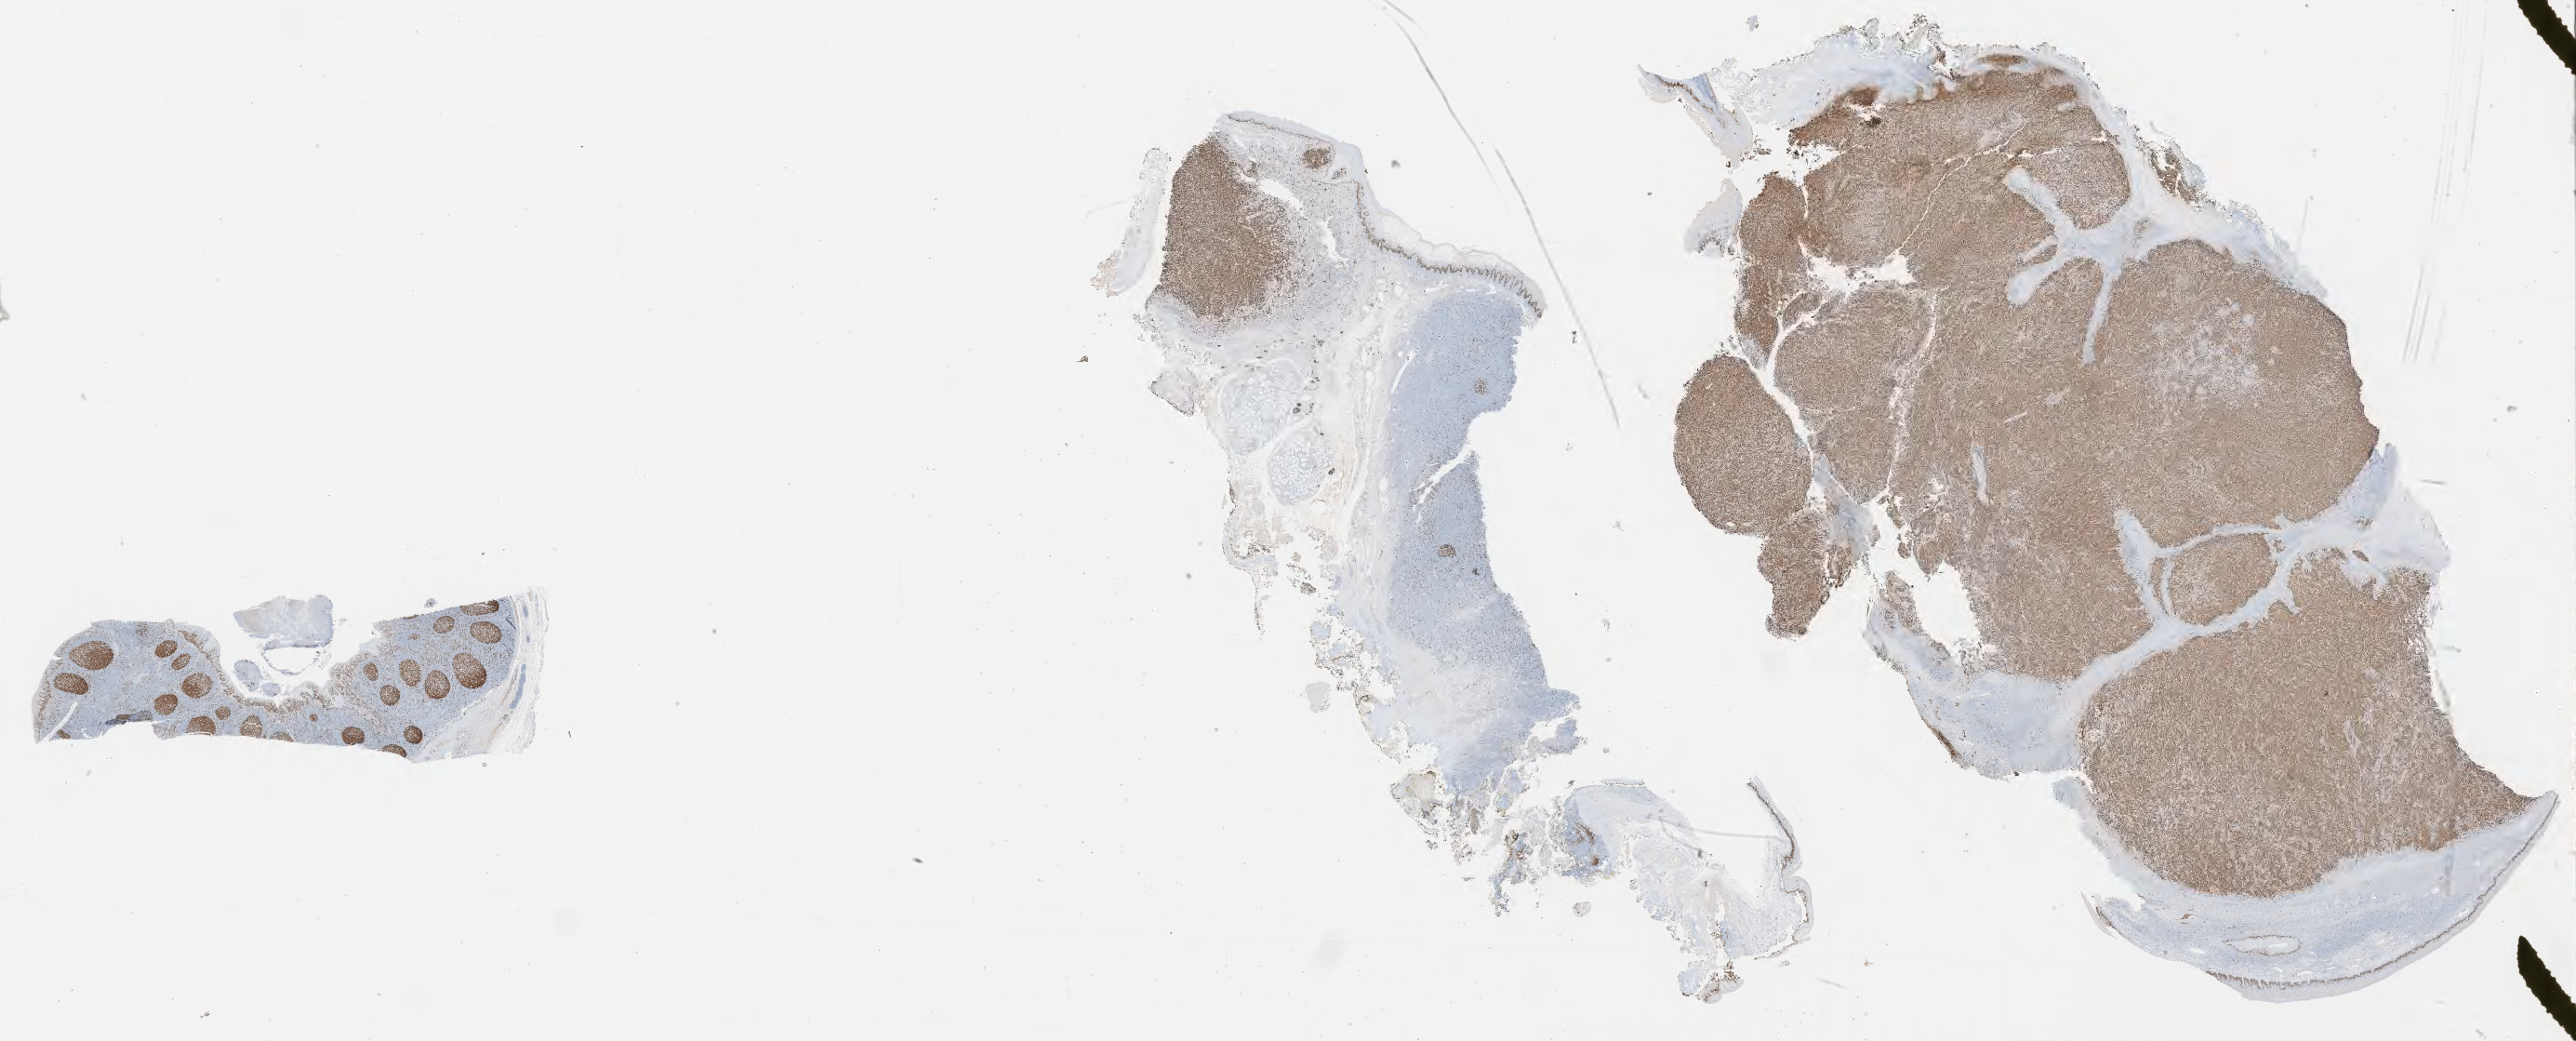
Immunohistochemistry (IHC) whole-slide image stained for Ki-67 — a low-resolution overview of the entire scanned area, about 44.8 x 18.1 mm. Tumor tissue. Anatomic site: lymph node. Patient: male, 56 years old.
Histologic diagnosis: Diffuse large B-cell lymphoma, NOS.